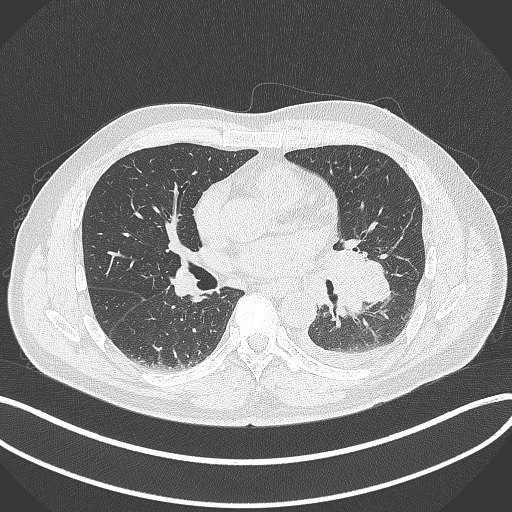
Chest CT, one axial slice; reconstruction kernel B70f; lung window (W 1500 / L -600 HU); 1 mm slice thickness; 512 × 512 image matrix, field of view 400 × 400 mm. Patient: male, 58 years. Case-level facts recorded for this patient, not image findings: clinical TNM (as recorded): T3 N1 M1b; histopathological grade: G3.
Outlined on this slice (bounding box drawn by a radiologist):
- lung tumour (recorded histology: small cell carcinoma): bounding box <317,240,397,318> (left, top, right, bottom; pixels)